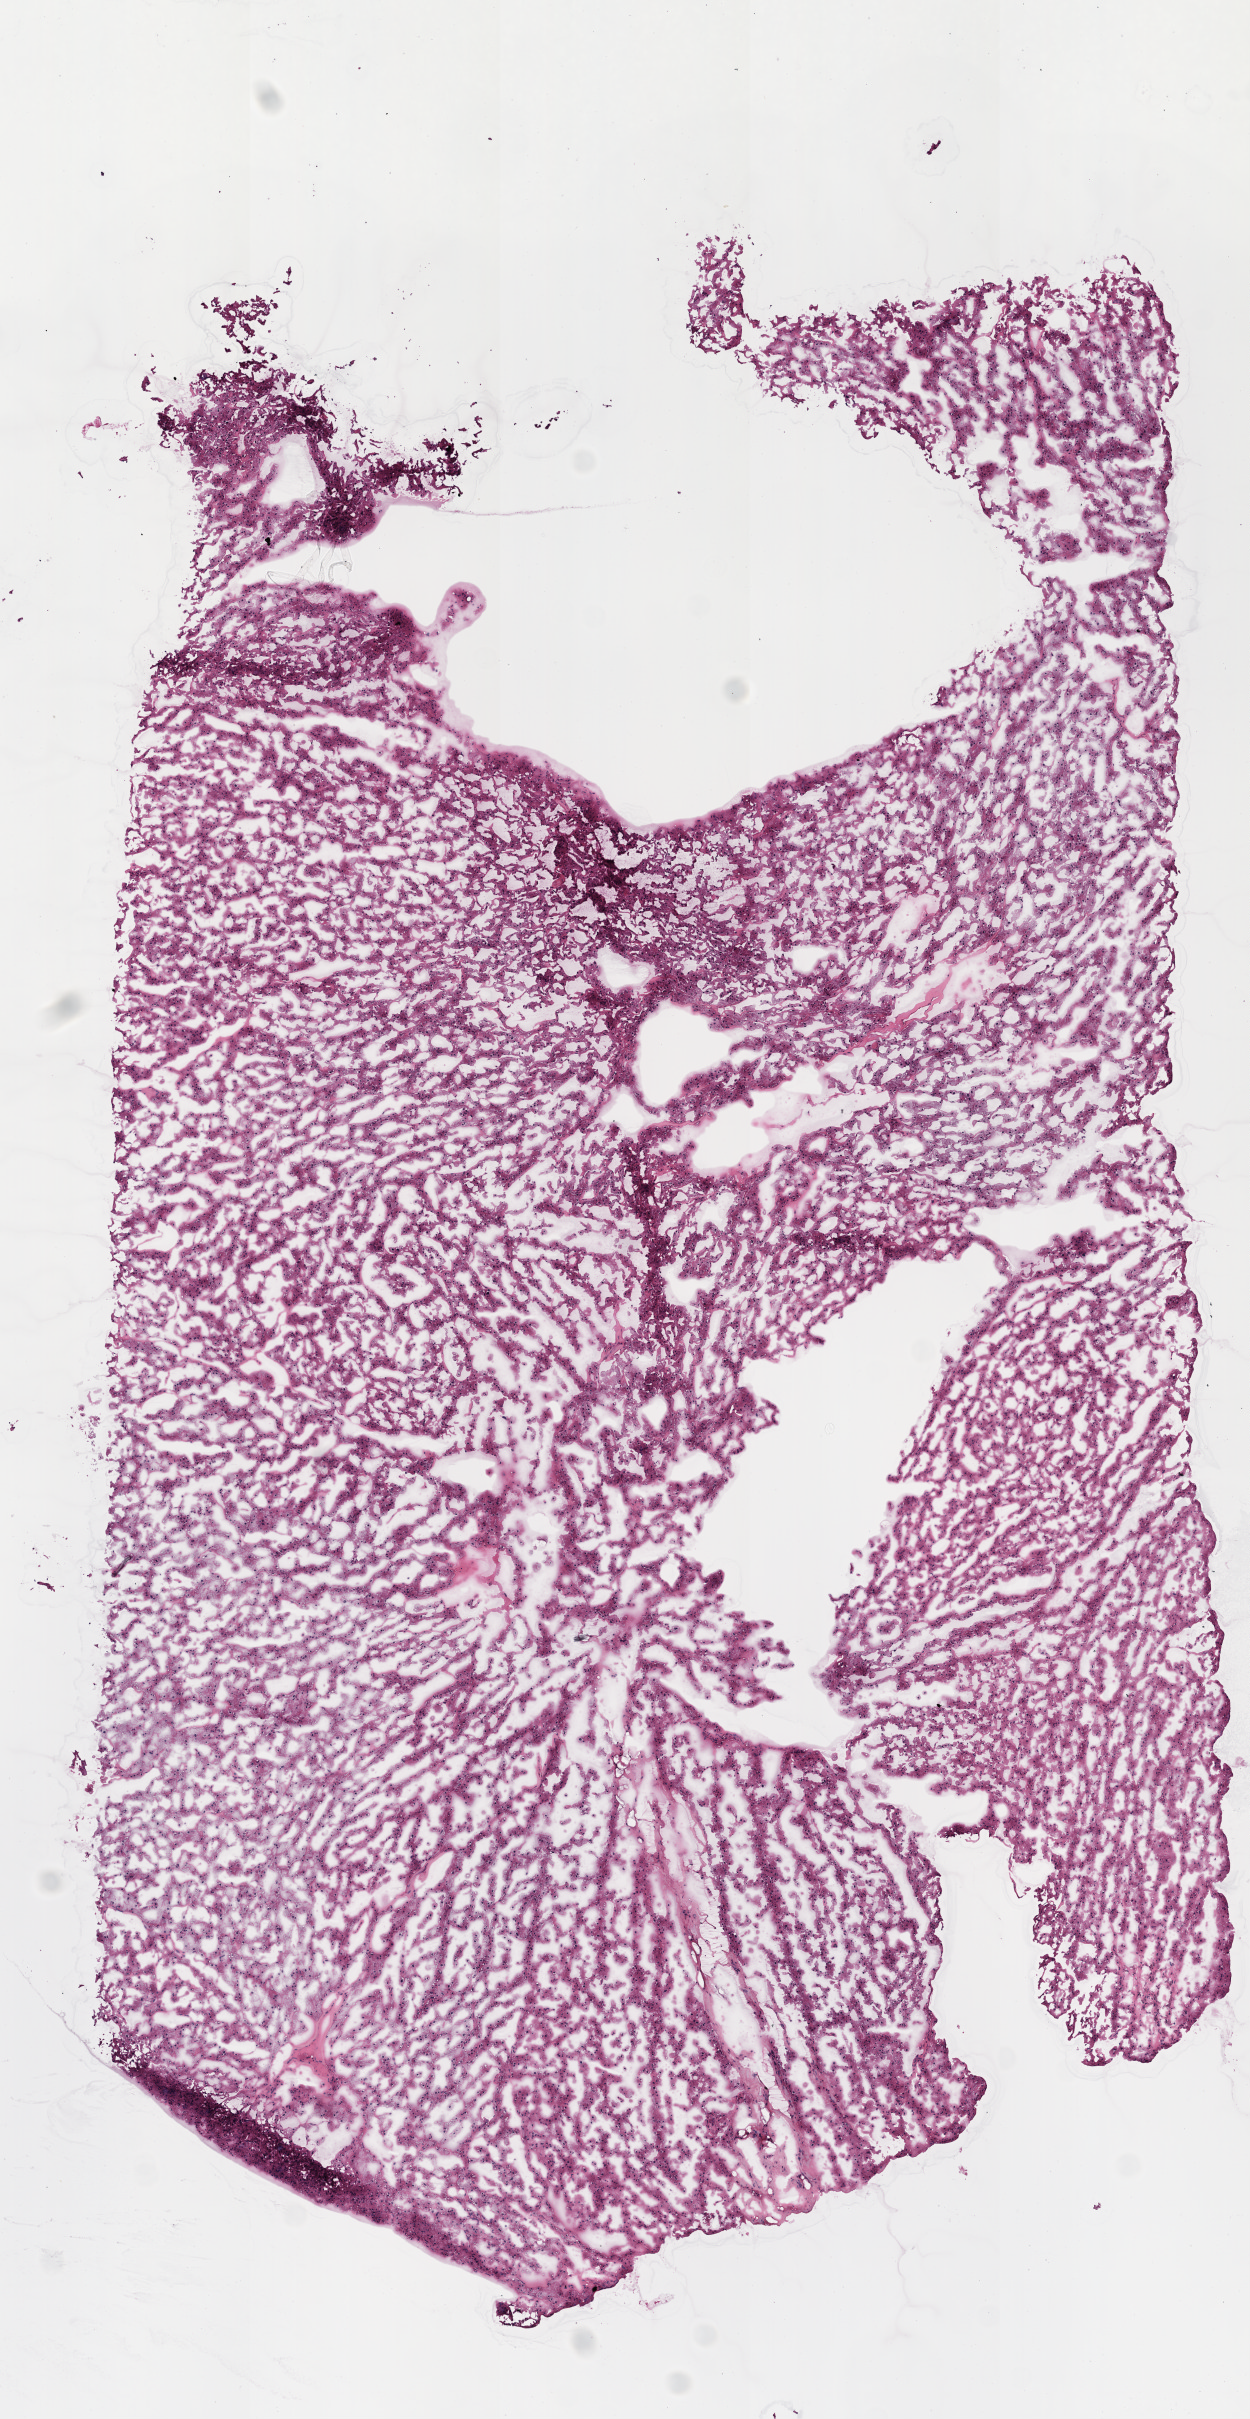
Digitized H&E-stained tissue section (whole slide), low-resolution overview of the scanned area, about 5.0 x 9.7 mm (slide scanned at 20x). Frozen section from the top of the tissue portion. Sample: primary tumour, kidney. Male patient; age at initial diagnosis 83 years. Histologic grade: G2 (moderately differentiated). Pathologist review of this section (percent, as recorded): tumour cells 95%, tumour nuclei 85%, normal cells 0%, stromal cells 5%, necrosis 0%.
• AJCC pathologic stage: II
• pathologic diagnosis: Clear cell adenocarcinoma, NOS